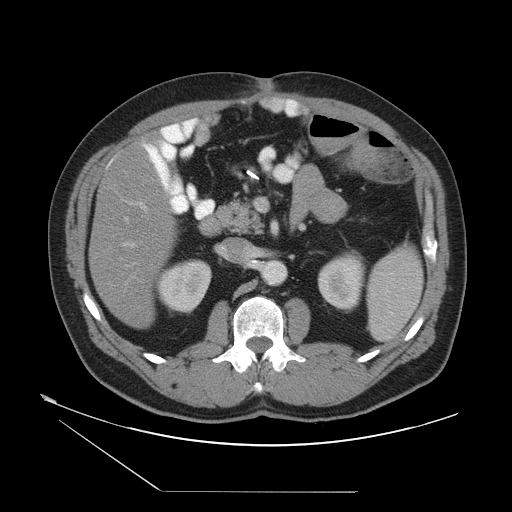
Contrast-enhanced abdominal CT, one axial slice. Slice 21 of 55 in the series (ordered by position). 120 kVp. Intravenous contrast given. Soft-tissue window (W 400 / L 40 HU). 5 mm slice thickness. 512 × 512 image matrix, field of view 454 × 454 mm. Male patient, age 59 years. Case-level facts recorded for this patient, not image findings: diagnosis: colorectal cancer liver metastases, imaged before liver resection; multiple liver metastases: yes.
Outlined on this slice (outlined manually by an expert reader):
- hepatic veins: bounding box <119,217,135,265> (left, top, right, bottom; pixels)
- liver: <90,148,171,327>
- planned liver remnant (the part of the liver to remain after resection): <90,148,171,327>
- portal vein (with intrahepatic branches): <122,201,147,248>